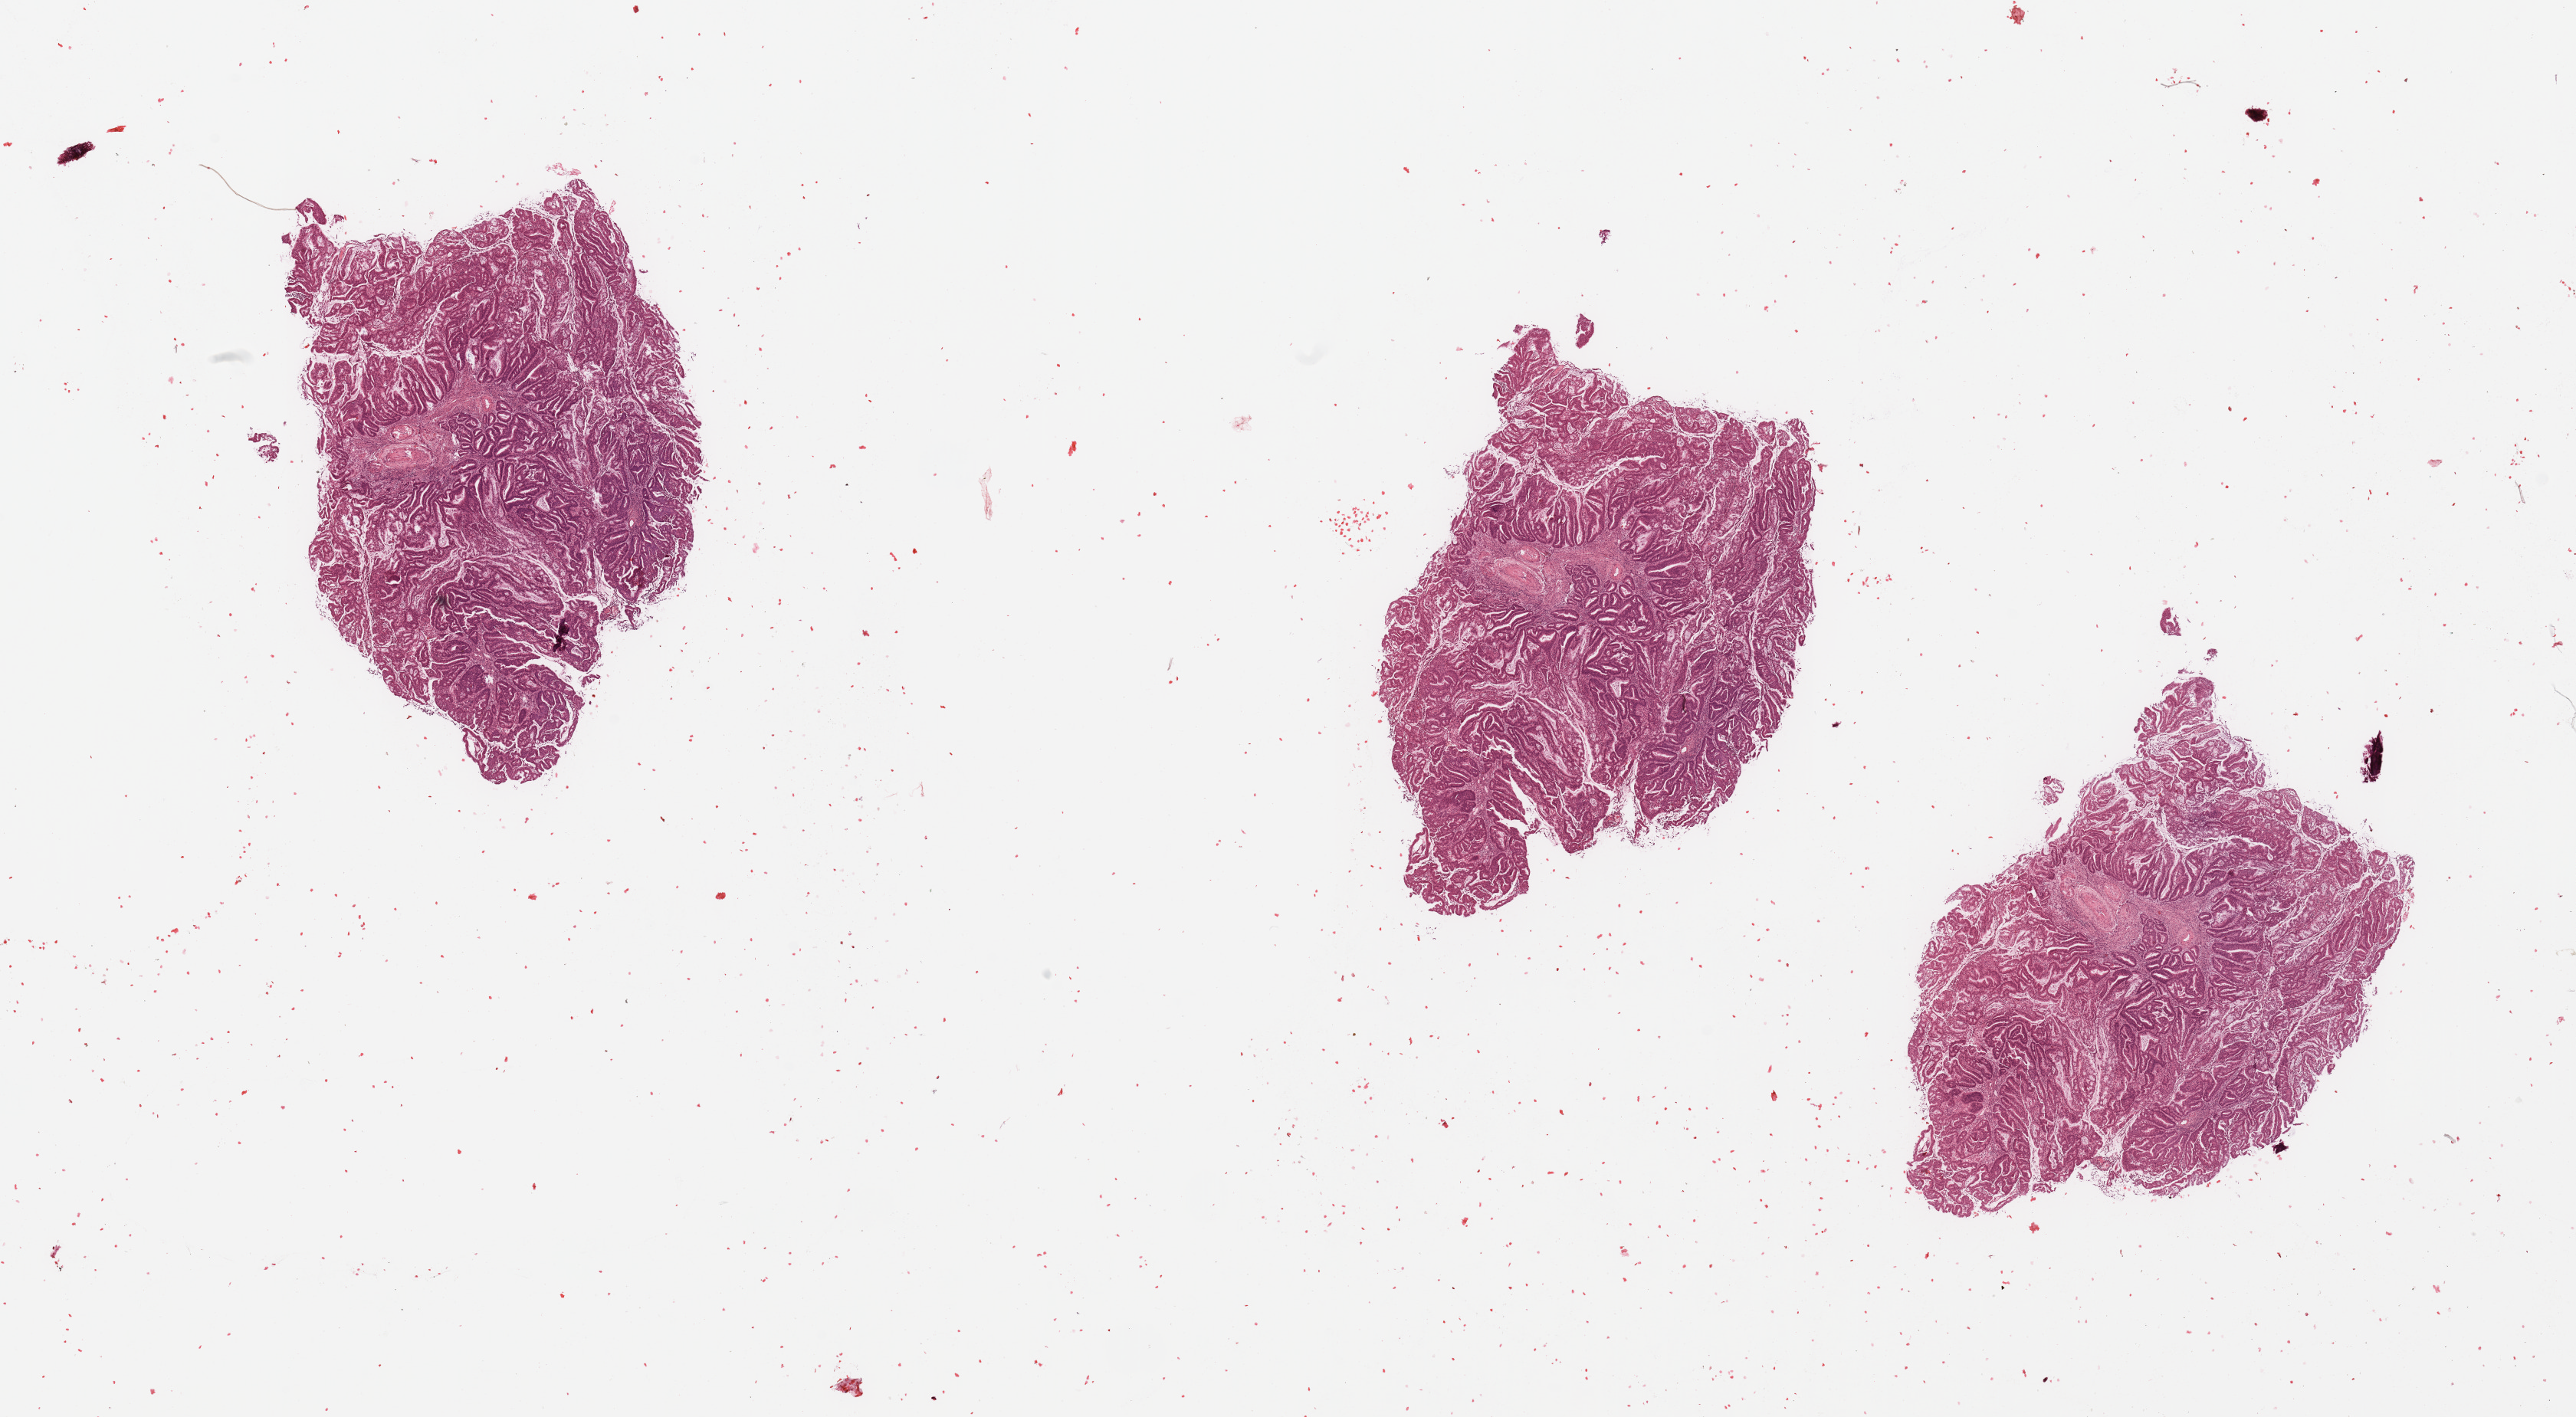
Hematoxylin and eosin (H&E) stained whole-slide image, shown as a low-resolution overview of the whole scanned area (about 26.6 x 14.6 mm), tumour tissue sample, sampled site: uterus. Patient: female, age 57 years. Histologic grade: G2 (moderately differentiated). Slide review estimates, as recorded: tumour nuclei 90%, necrosis 2%.
Diagnosis: Endometrioid adenocarcinoma, NOS. Primary tumour site (as recorded): posterior endometrium. AJCC pathologic stage: I.